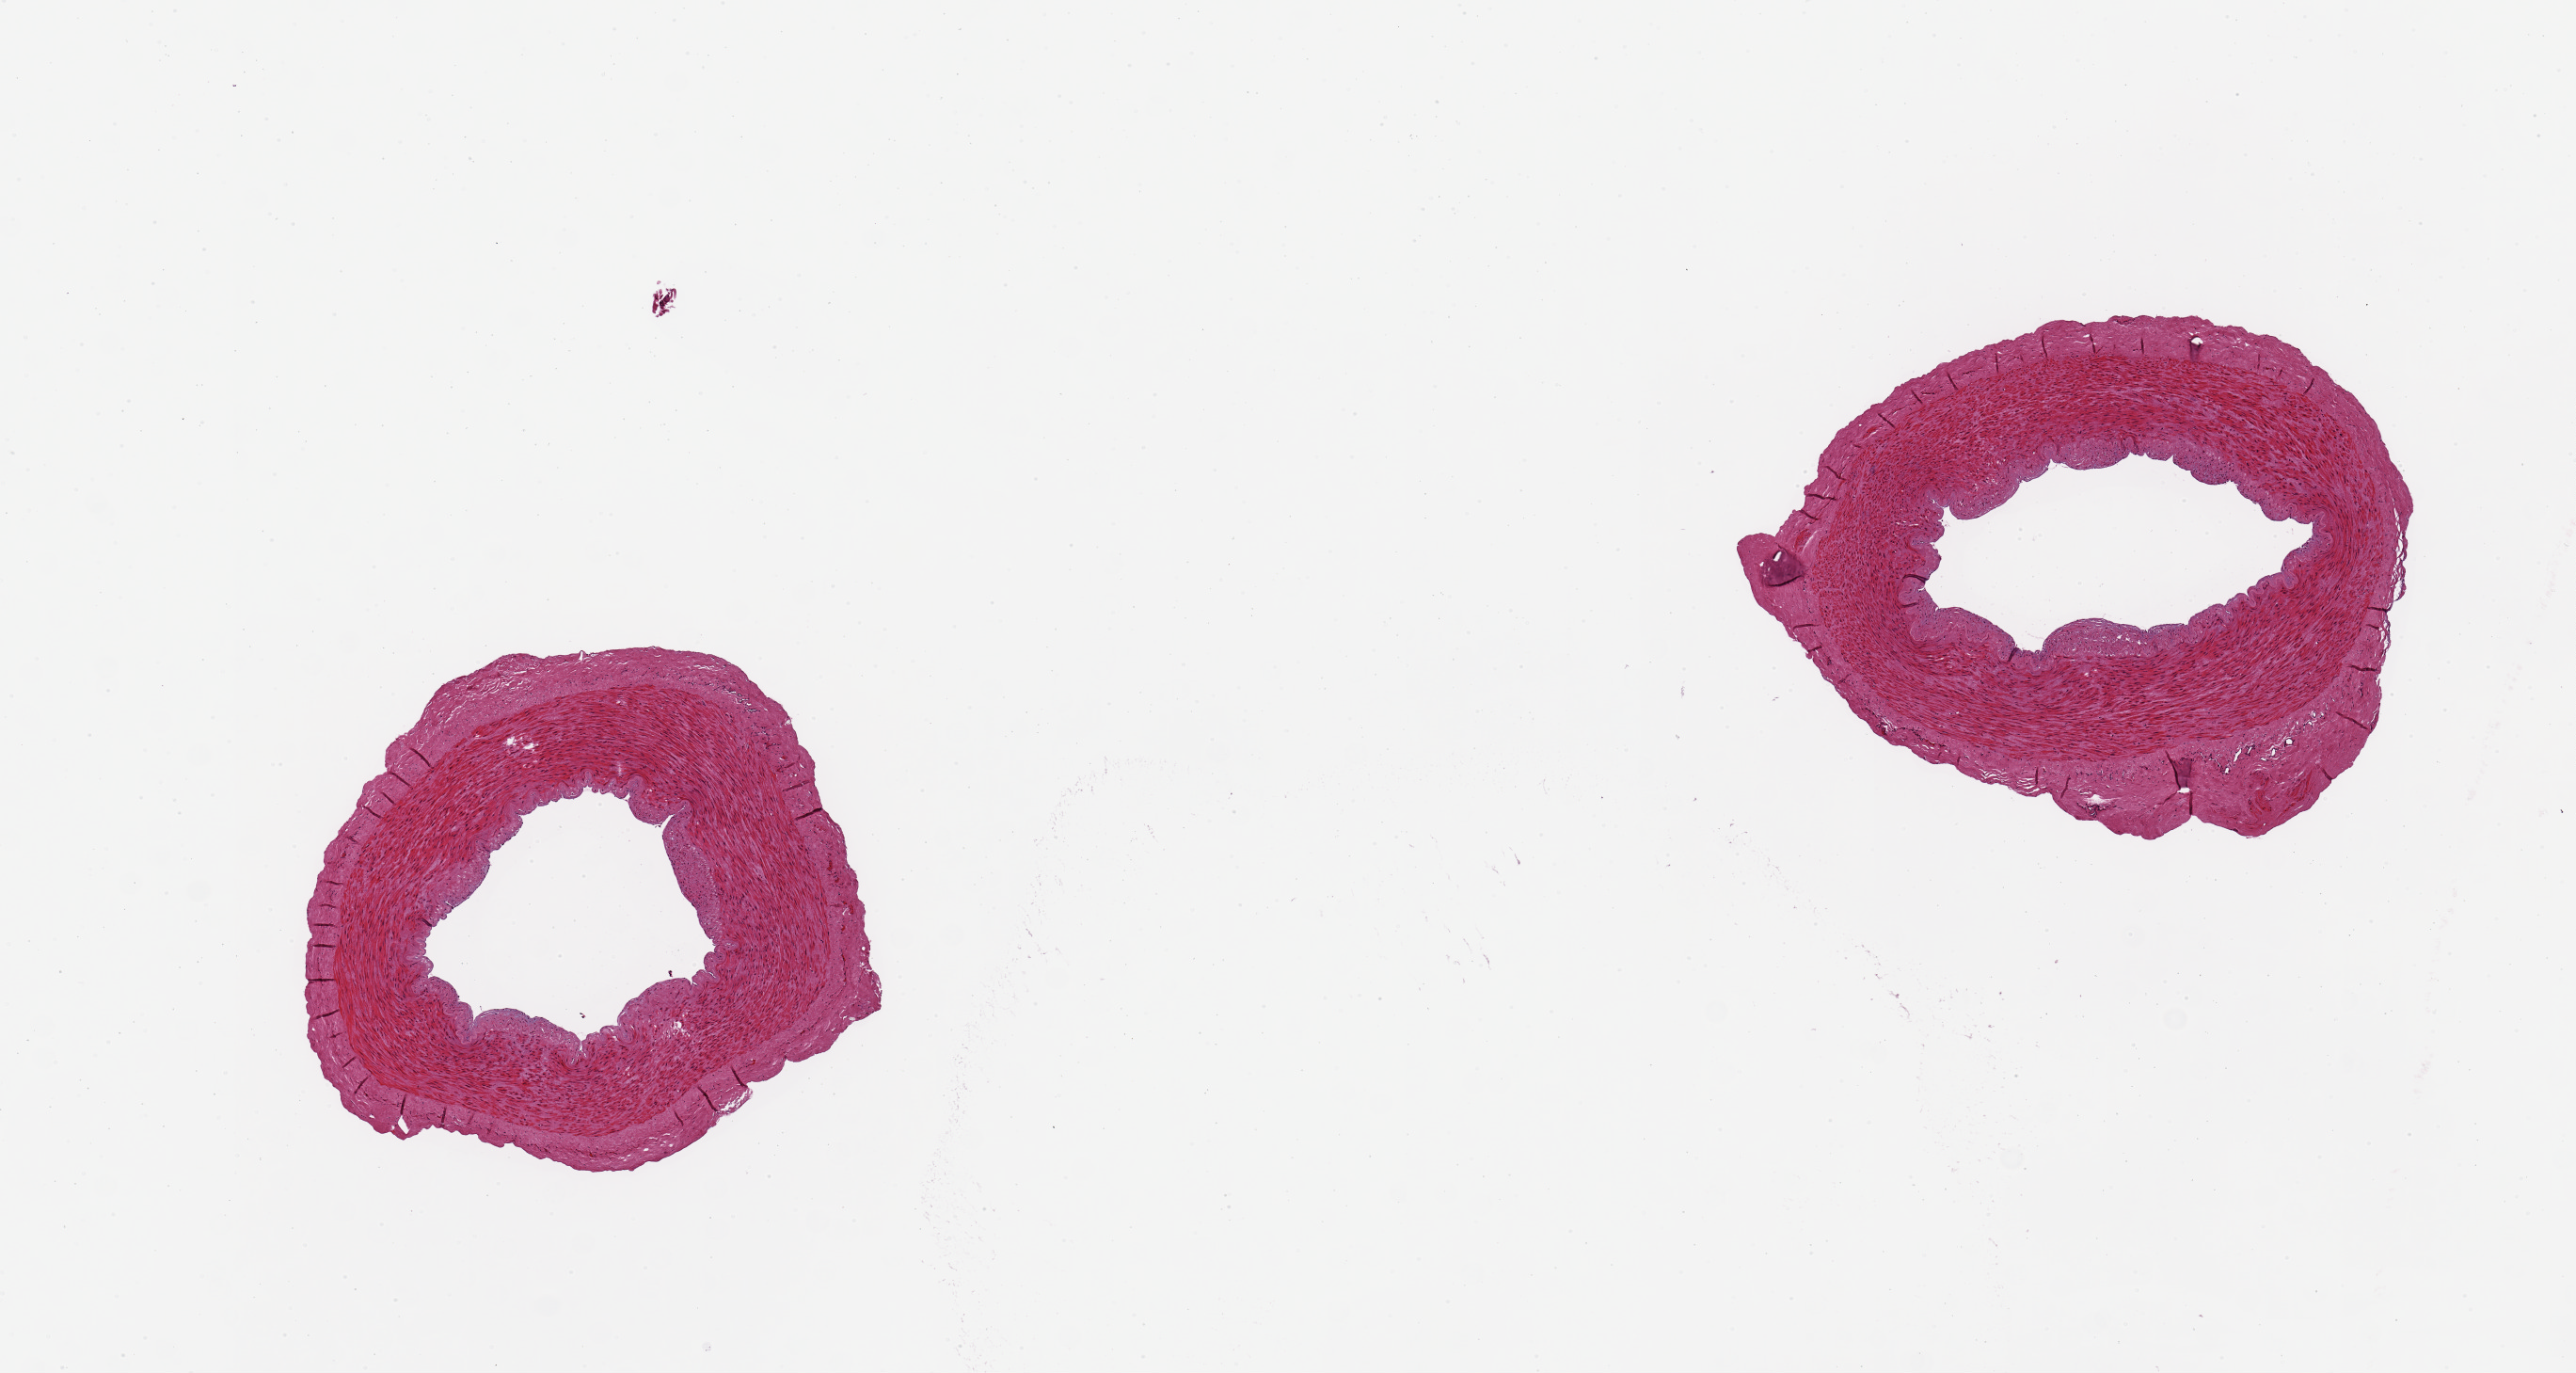
Hematoxylin and eosin (H&E) whole-slide image, low-resolution overview of the scanned area, about 10.8 x 5.8 mm; PAXgene-fixed paraffin-embedded (PFPE) section; section of tibial artery (target tissue); tissue donor sample. Donor sex: male.
Reviewer comment on this tissue sample: 2 pieces, ~2.5mm d. Good clean specimen.